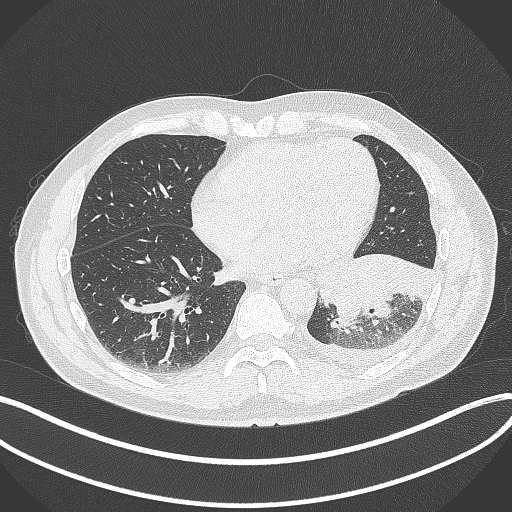
Chest CT, one axial slice; position 125 of 342 along the scan axis; 120 kVp; lung window (W 1500 / L -600 HU); 1 mm slice thickness; 512 × 512 image matrix. Patient: male, 58 years. Case-level facts recorded for this patient, not image findings: clinical TNM (as recorded): T3 N1 M1b; histopathological grade: G3.
Structures marked on this image (rectangle marked by the reading radiologist):
- lung tumour (recorded histology: small cell carcinoma): box from (x=316, y=246) to (x=436, y=327) px